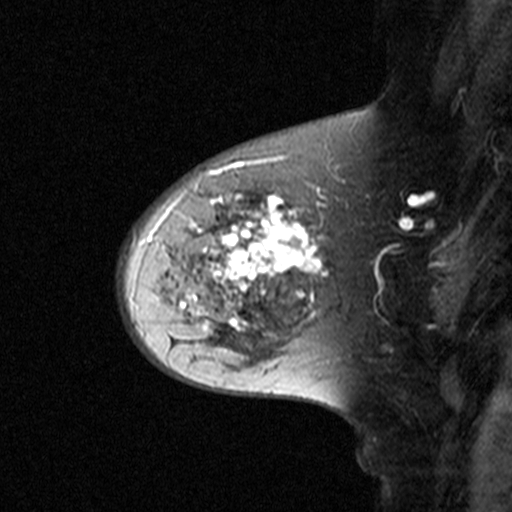
Breast MRI (dynamic contrast-enhanced), one sagittal slice; slice 30 of 44 in the series (ordered by position); dynamic contrast-enhanced study with each time point stored as its own series, time point 2 of 3 at this slice position (early post-contrast, ordered by acquisition time); 1.5 T; TE 4.5 ms, TR 11 ms; 3 mm slice thickness; 512 × 512 image matrix. Patient: female, 65 years. Case-level facts recorded for this patient, not image findings: setting: breast cancer imaged before/during neoadjuvant chemotherapy; receptor status: HER2-positive.
Structures marked on this image (semi-automatic segmentation, software-assisted and operator-edited):
- analysis volume of interest (the breast-tissue region the enhancement analysis was run in; not a lesion): bounding box [x1, y1, x2, y2] px = [160, 172, 329, 345]
- tumour enhancement mask (voxels above the 90 % enhancement threshold inside the analysis volume of interest): [167, 172, 328, 331]